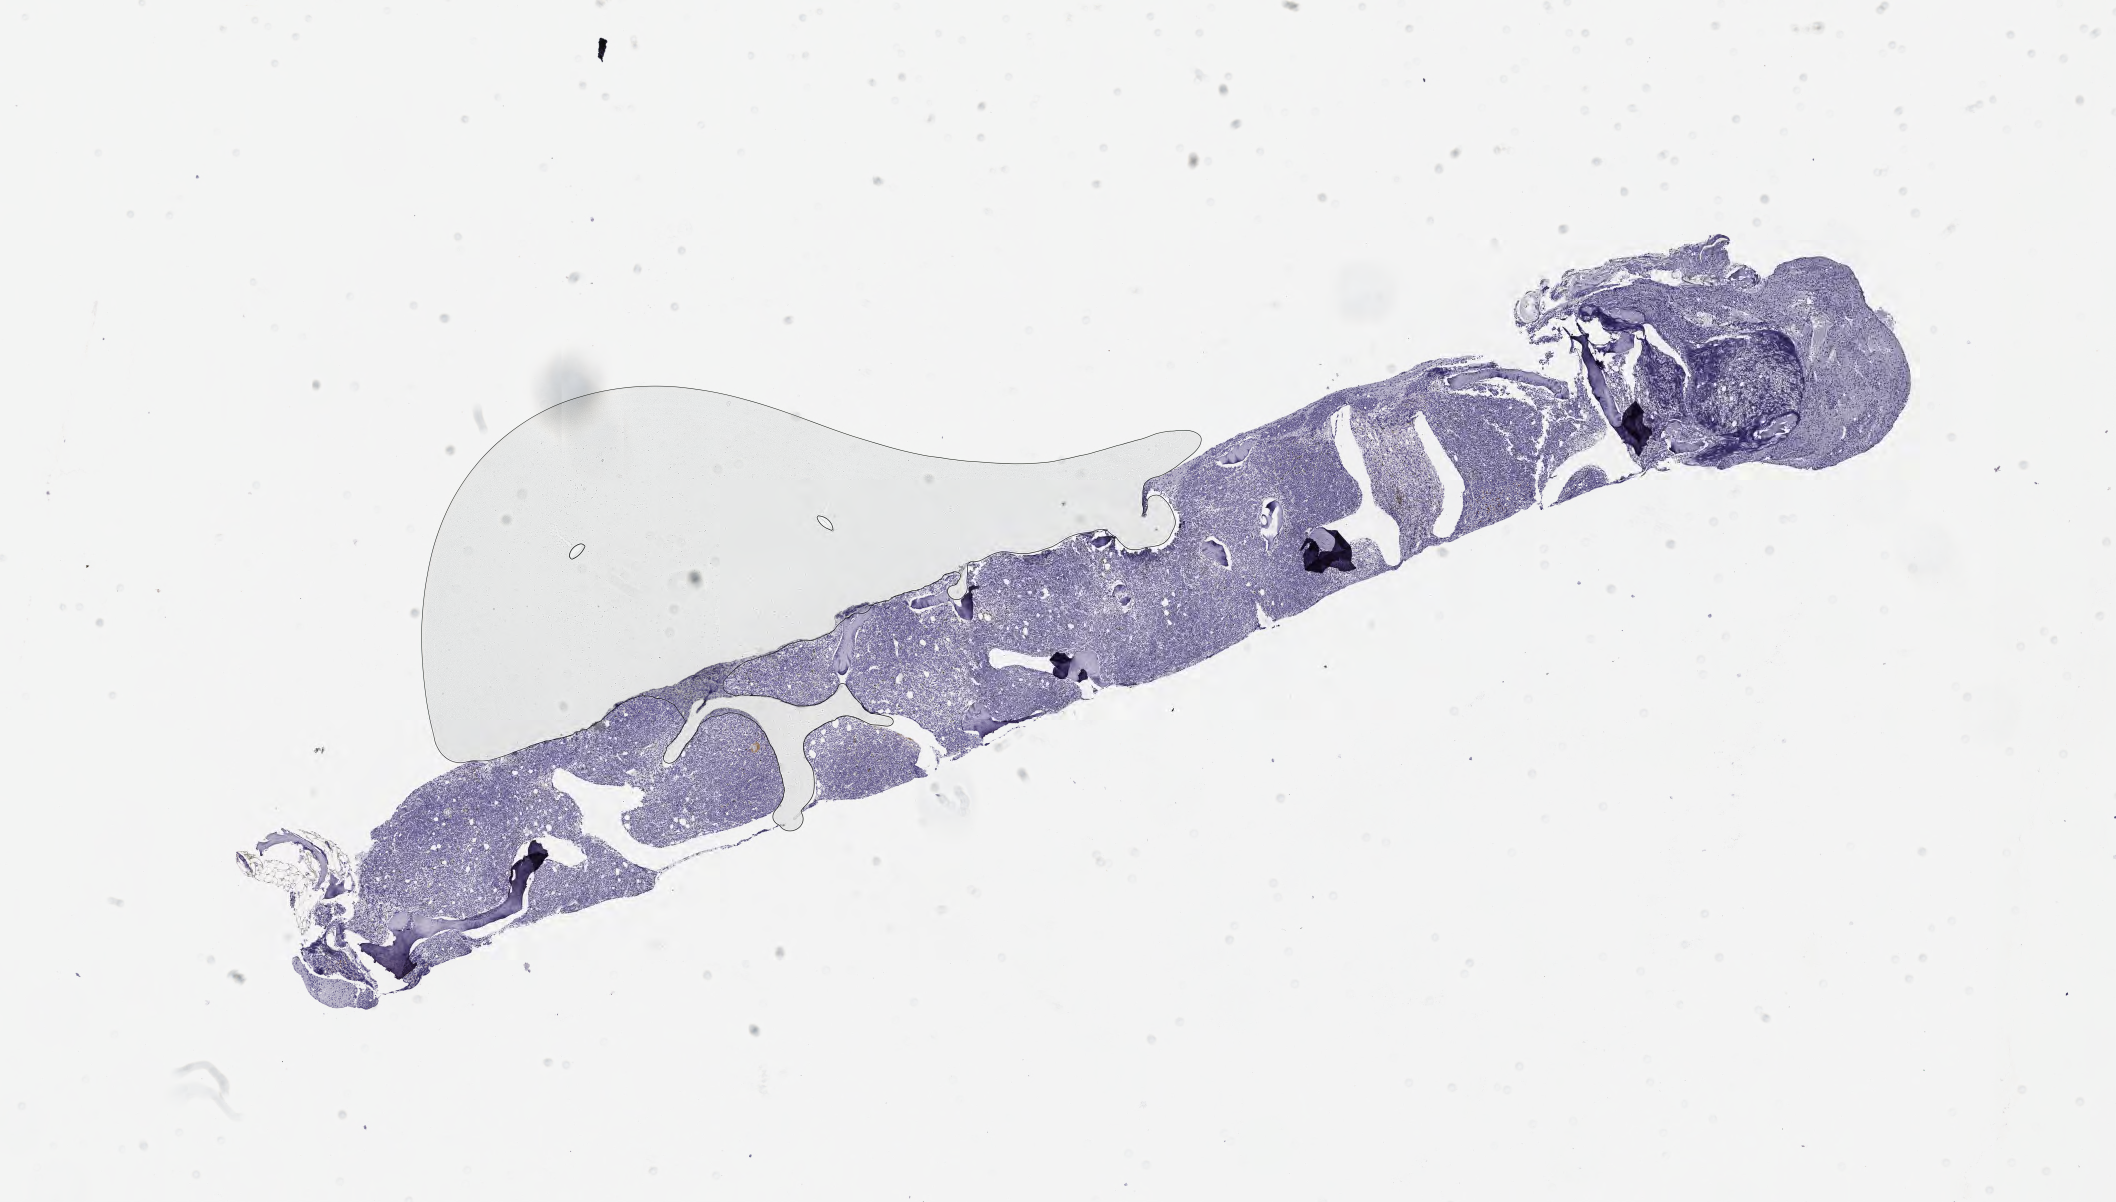
IHC for BCL2, whole-slide image, whole scanned area (about 17.1 x 9.7 mm) shown as a low-resolution overview, specimen: tumor tissue. Patient: female, aged 64.
Diagnosis: Burkitt lymphoma, NOS.